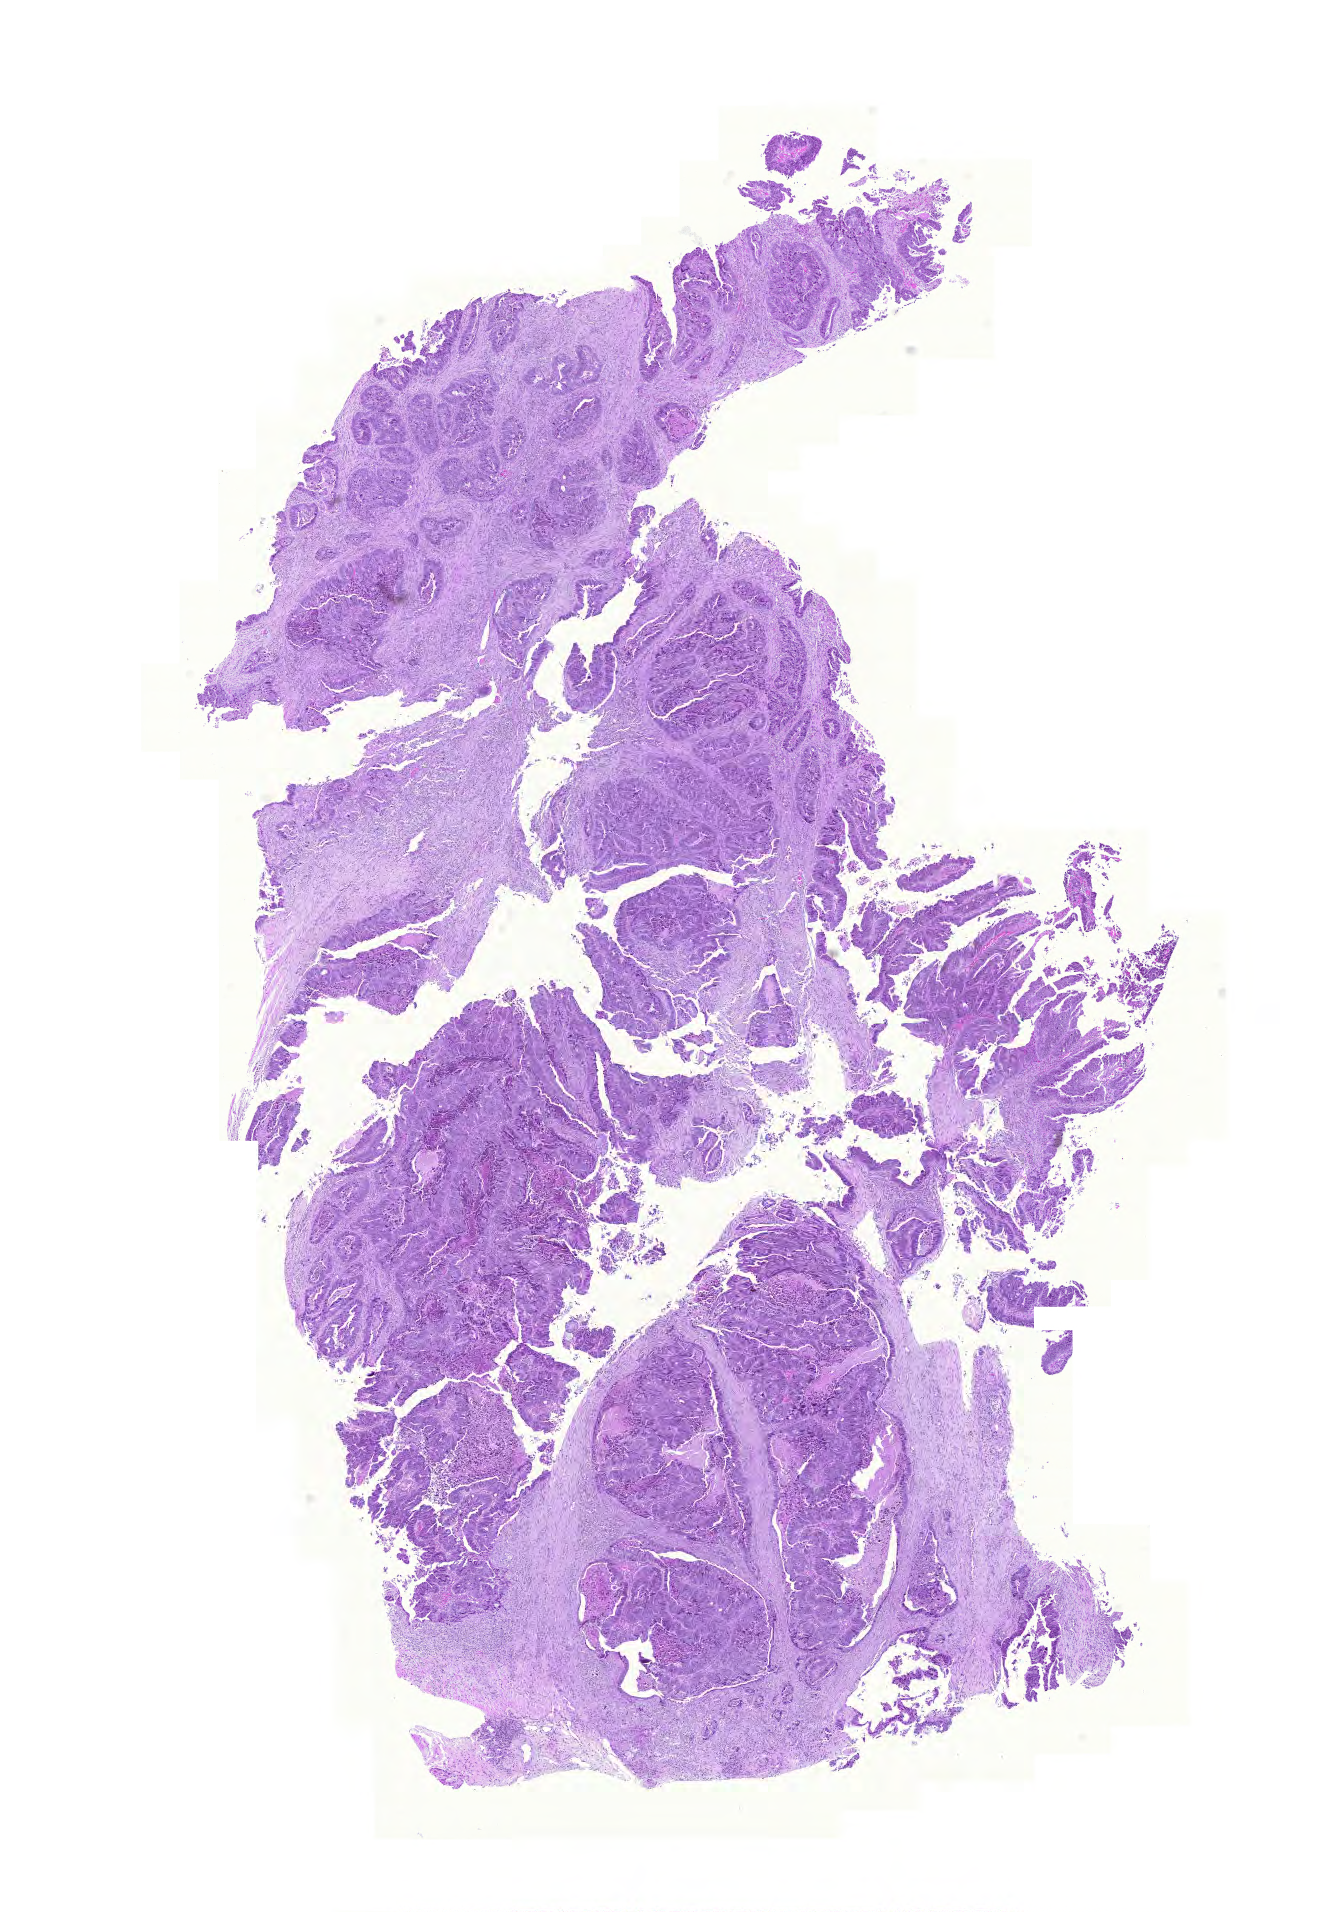
H&E whole-slide image, low-resolution overview of the scanned area, about 9.9 x 14.2 mm. Formalin-fixed paraffin-embedded (FFPE) diagnostic section. Rectum, primary tumour sample. Male, age 61 years at initial diagnosis.
* lymph nodes positive (case pathology): 0 of 21 examined
* AJCC pathologic stage: IIA (6th edition)
* histologic diagnosis: Adenocarcinoma, NOS